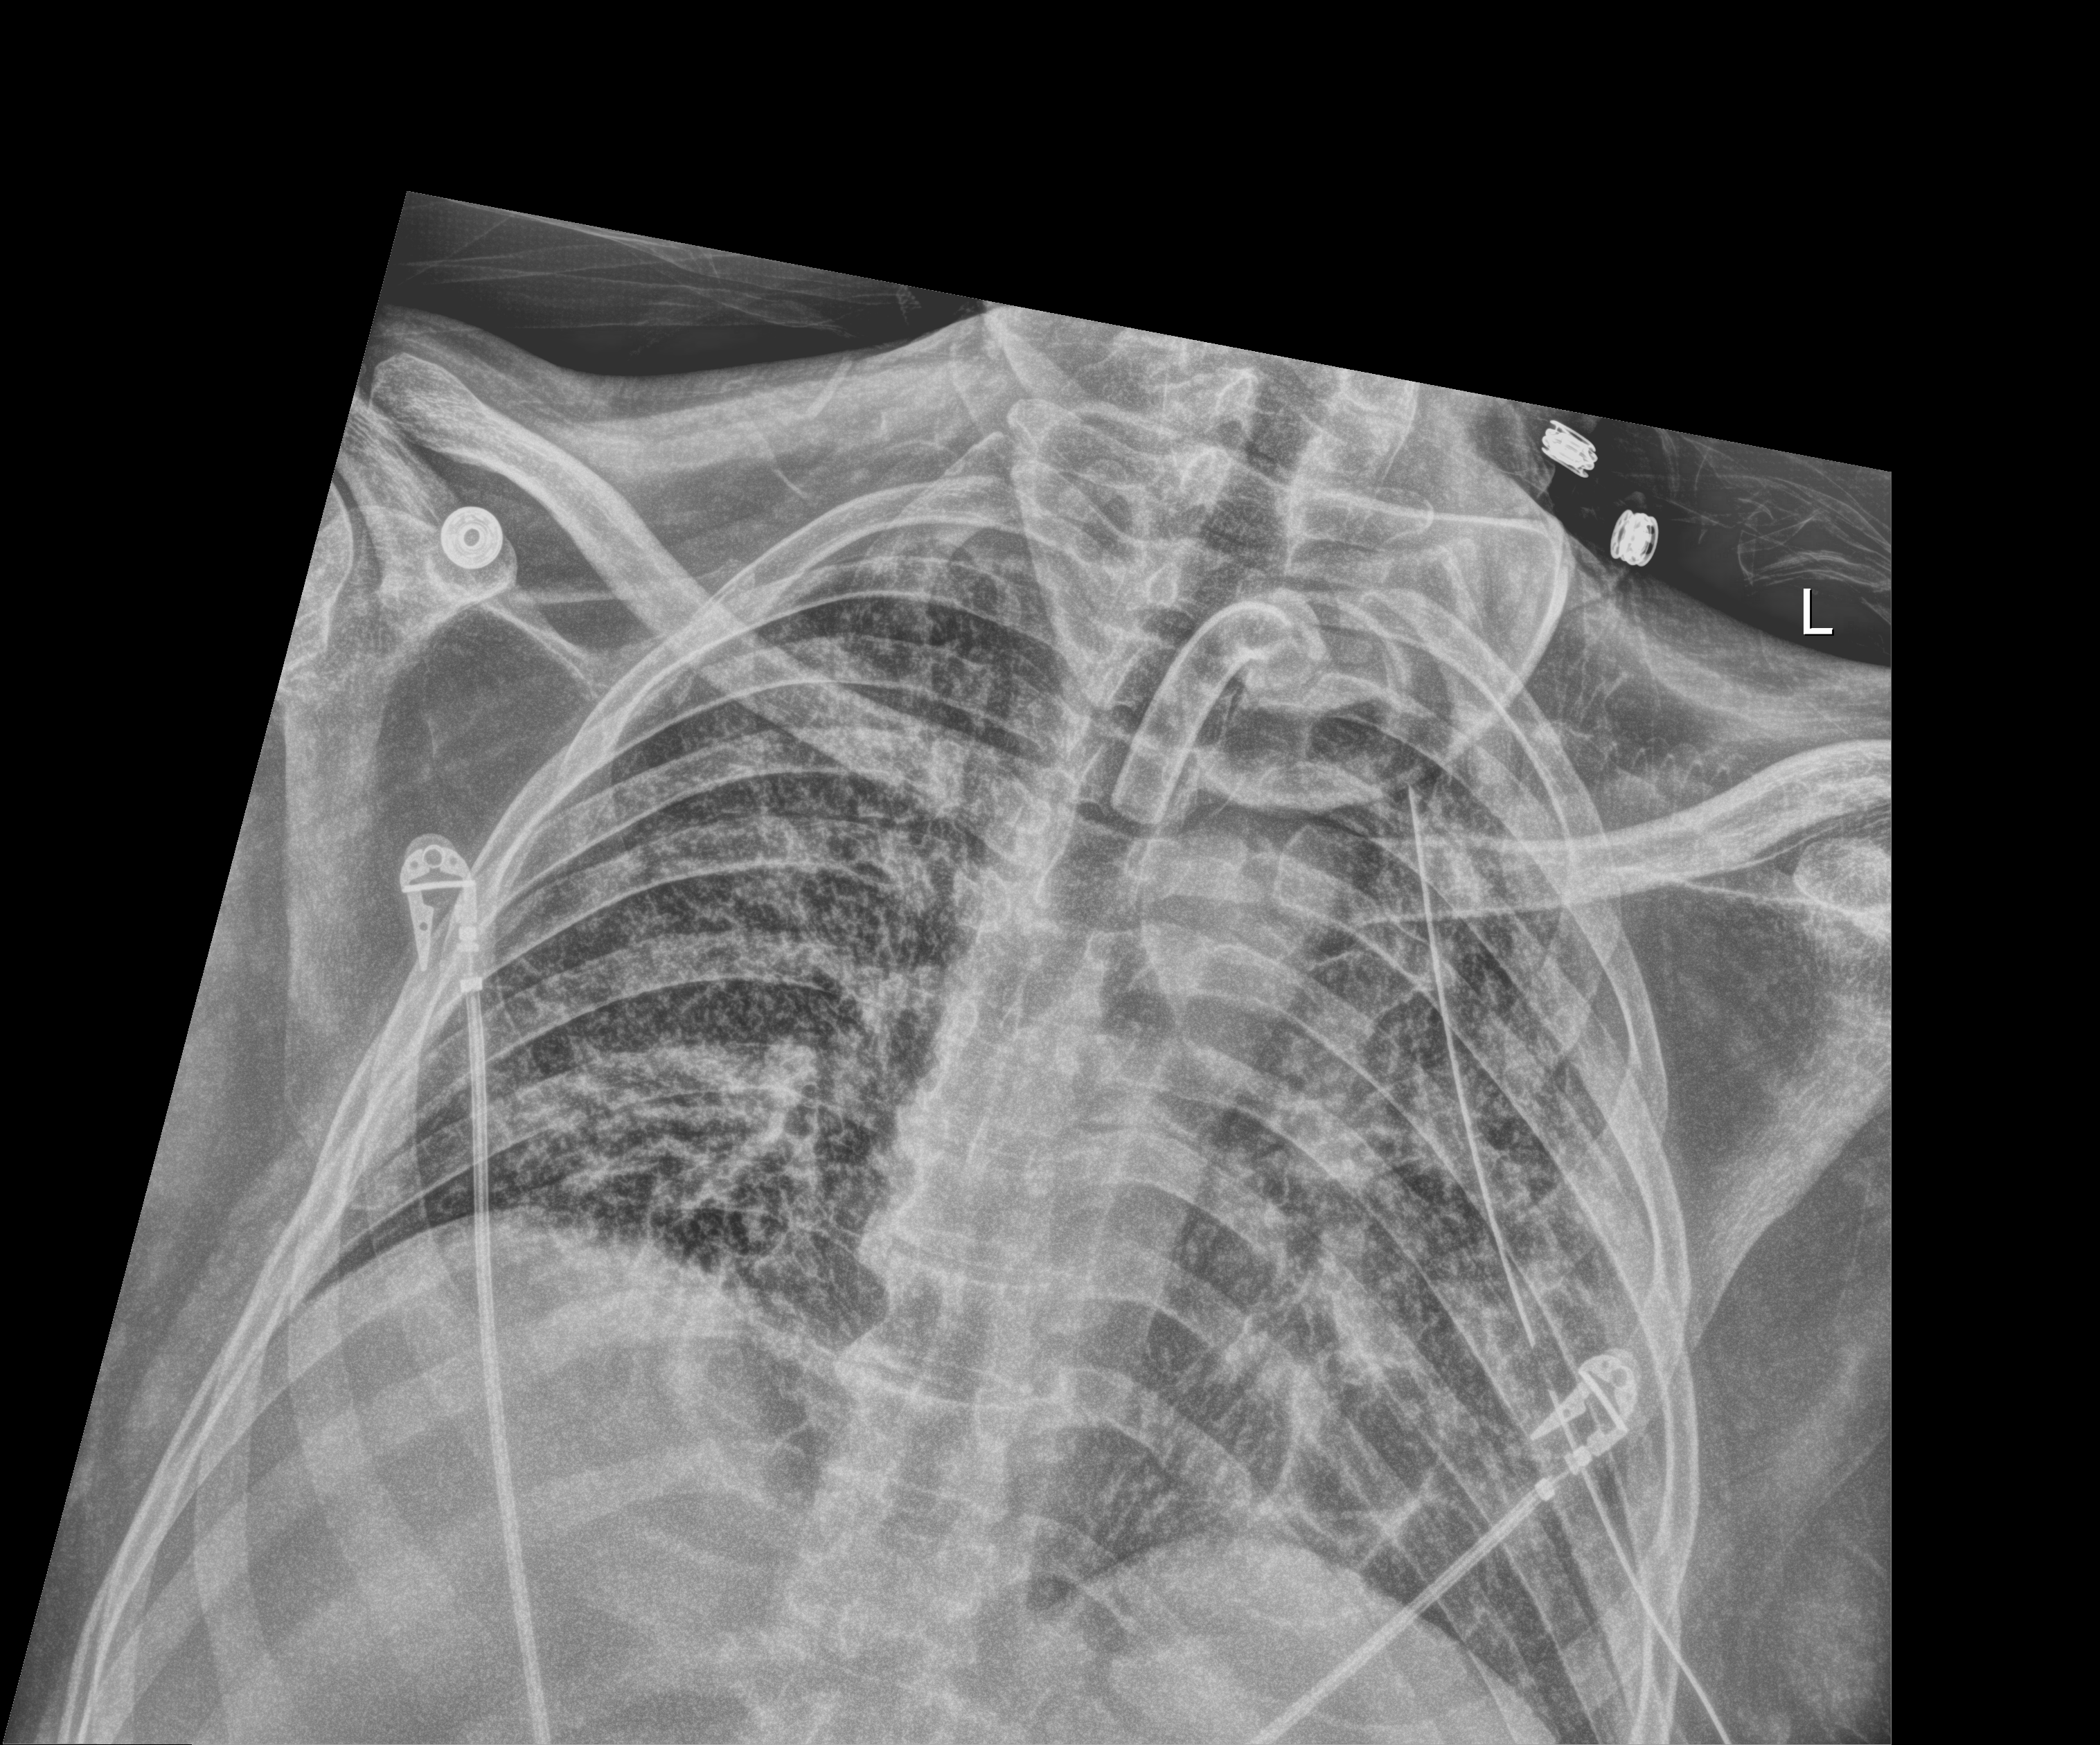
Chest X-ray (portable); anteroposterior (AP) projection. Patient hospitalised with COVID-19; male, aged 18–59 years.
From the hospital-stay record, not from the radiograph (when in the stay this image was taken is not recorded):
- chronic kidney disease (admission record): no